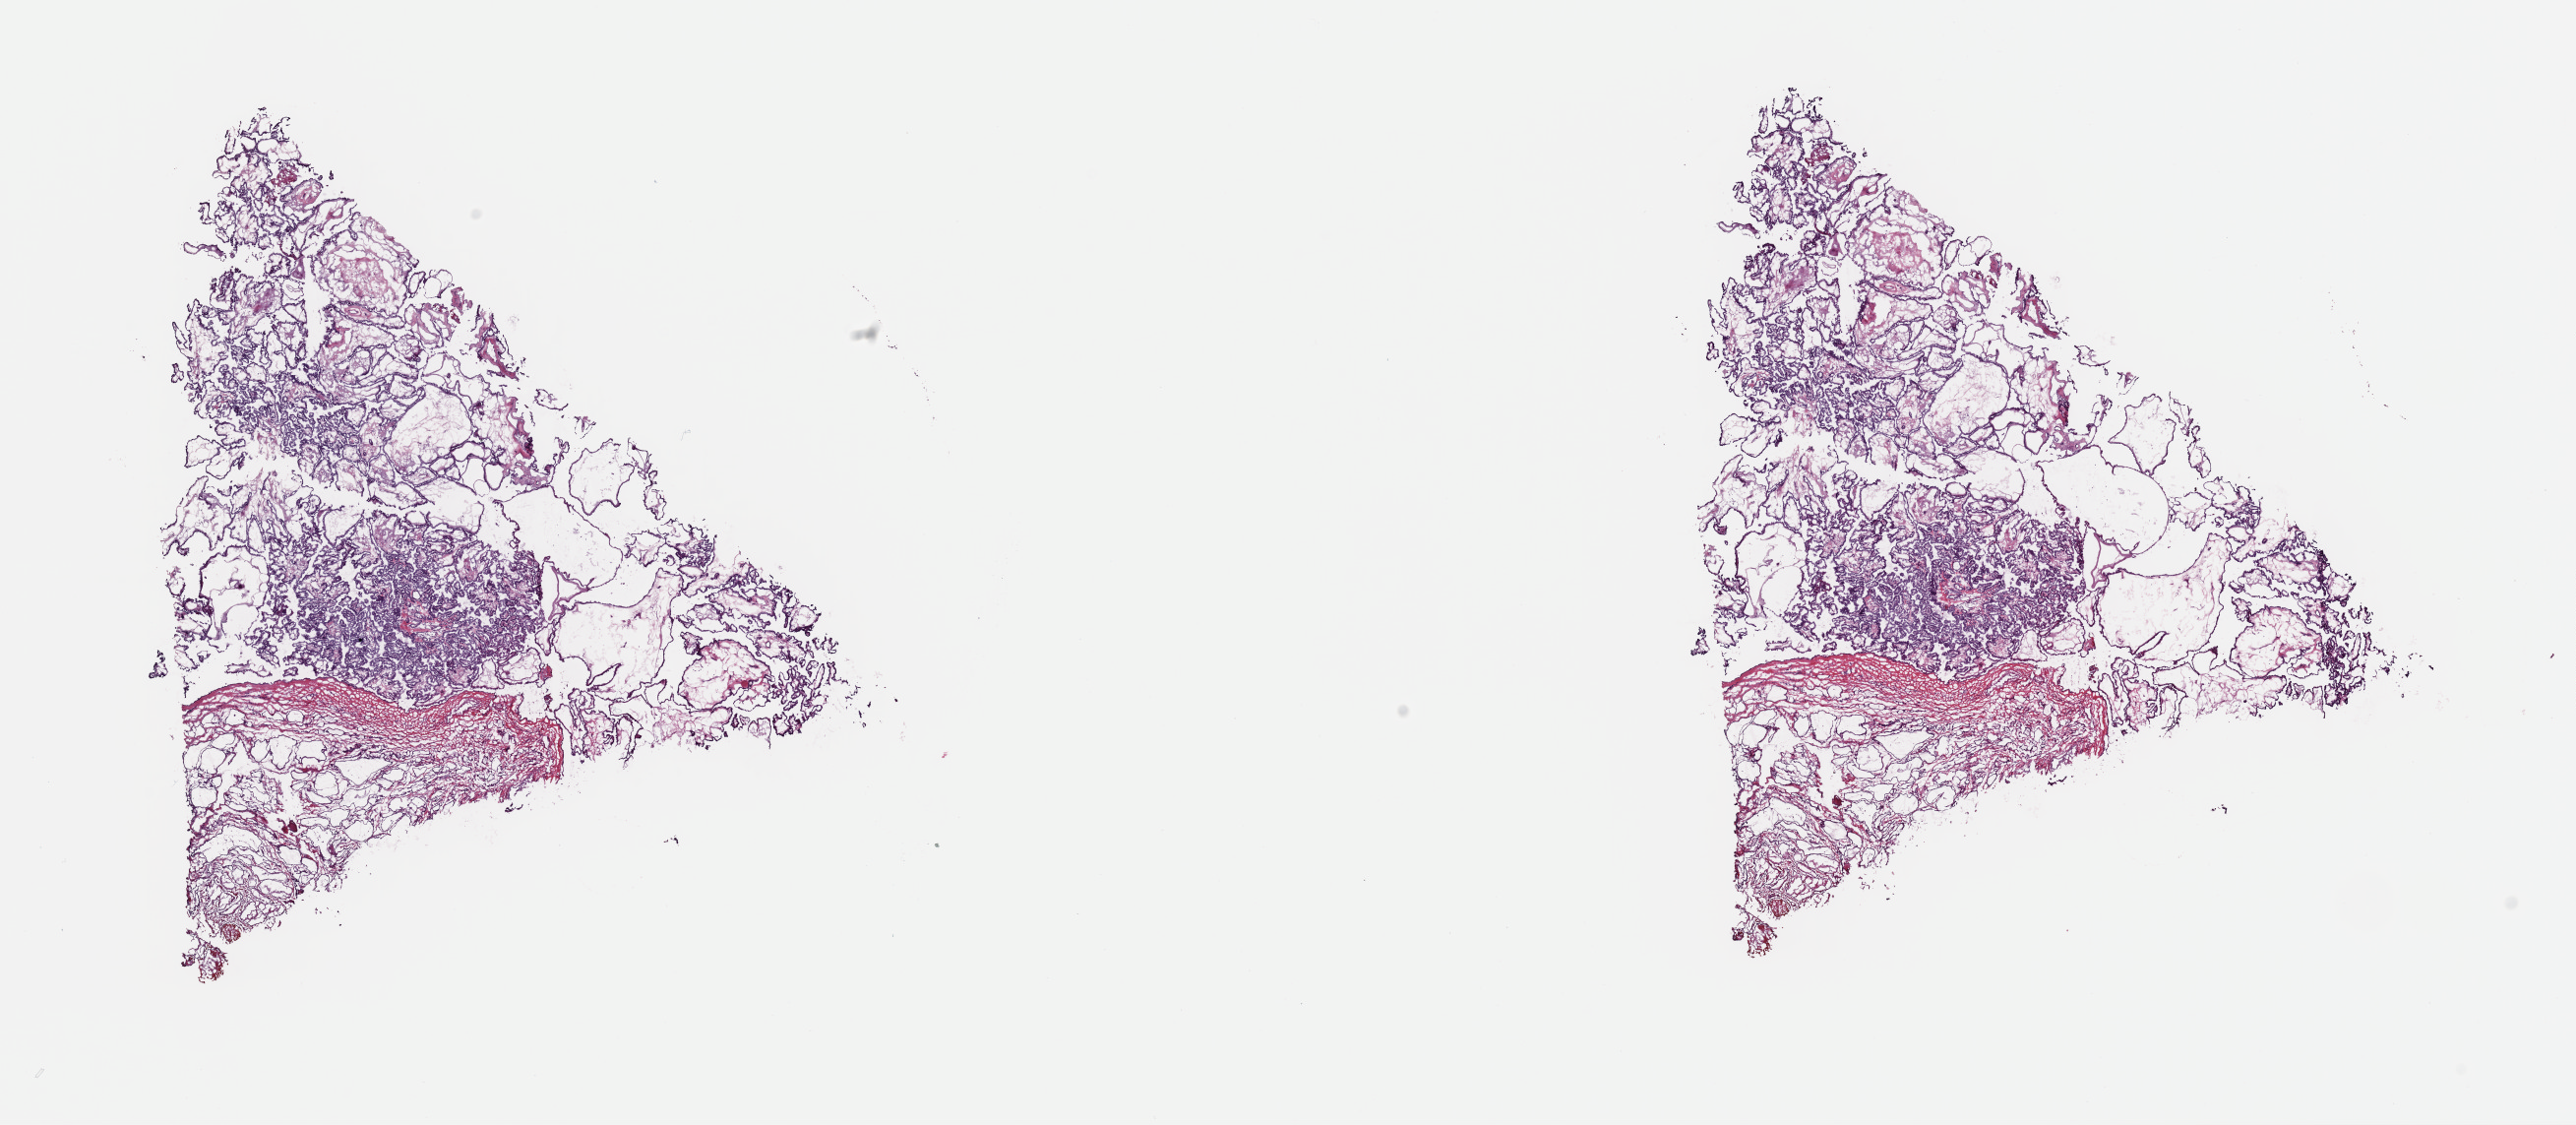
Digitized H&E-stained tissue section (whole slide) — shown as a low-resolution overview of the whole scanned area (about 20.7 x 9.0 mm); frozen section from the top of the tissue portion; thyroid, primary tumour sample. Female patient; age at initial diagnosis 33 years. Pathologist review of this section (percent, as recorded): tumour cells 80%, tumour nuclei 80%, normal cells 6%, stromal cells 14%, necrosis 0%. Inflammatory infiltration, as recorded: lymphocyte infiltration 2%, monocyte infiltration 1%, neutrophil infiltration 0%.
- laterality: right
- TNM: T2 NX MX
- diagnosis: Papillary adenocarcinoma, NOS
- AJCC pathologic stage: I